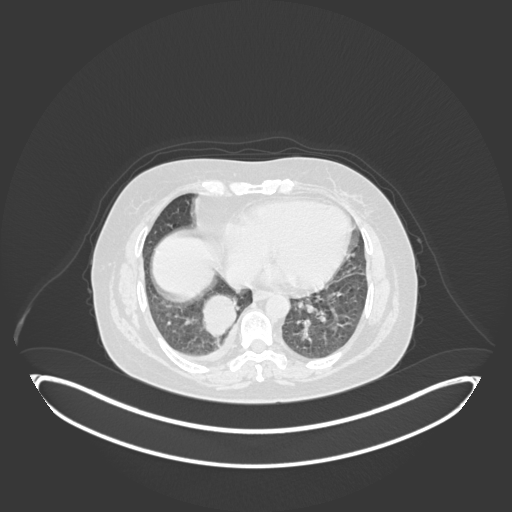
Chest CT, one axial slice. Lung window (W 1500 / L -600 HU). 1 mm slice thickness. 512 × 512 image matrix, field of view 500 × 500 mm. Female patient, age 56 years. Case-level facts recorded for this patient, not image findings: clinical TNM (as recorded): T2b N1 M0.
Outlined on this slice (bounding box drawn by a radiologist):
- lung tumour (recorded histology: small cell carcinoma): bounding box [x1, y1, x2, y2] px = [202, 292, 245, 340]